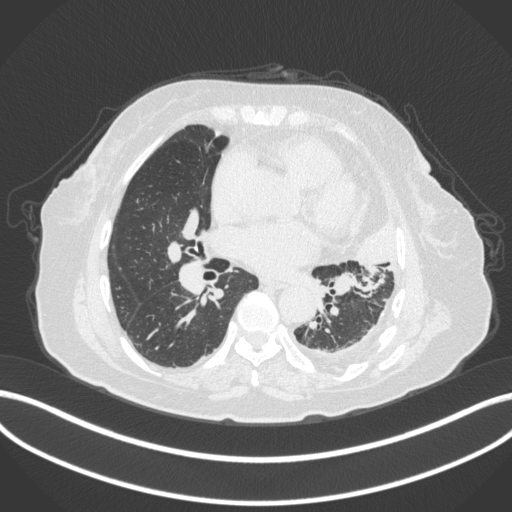
Chest CT, one axial slice. Slice 176 of 399 in the series (ordered by position). Reconstruction kernel B31f. Lung window (W 1500 / L -600 HU). 1 mm slice thickness. 512 × 512 image matrix, field of view 400 × 400 mm. Patient: female, 75 years. Case-level facts recorded for this patient, not image findings: clinical TNM (as recorded): T3 N3 M1.
Outlined on this slice (rectangle marked by the reading radiologist):
- lung tumour (recorded histology: adenocarcinoma): box from (x=352, y=220) to (x=404, y=274) px